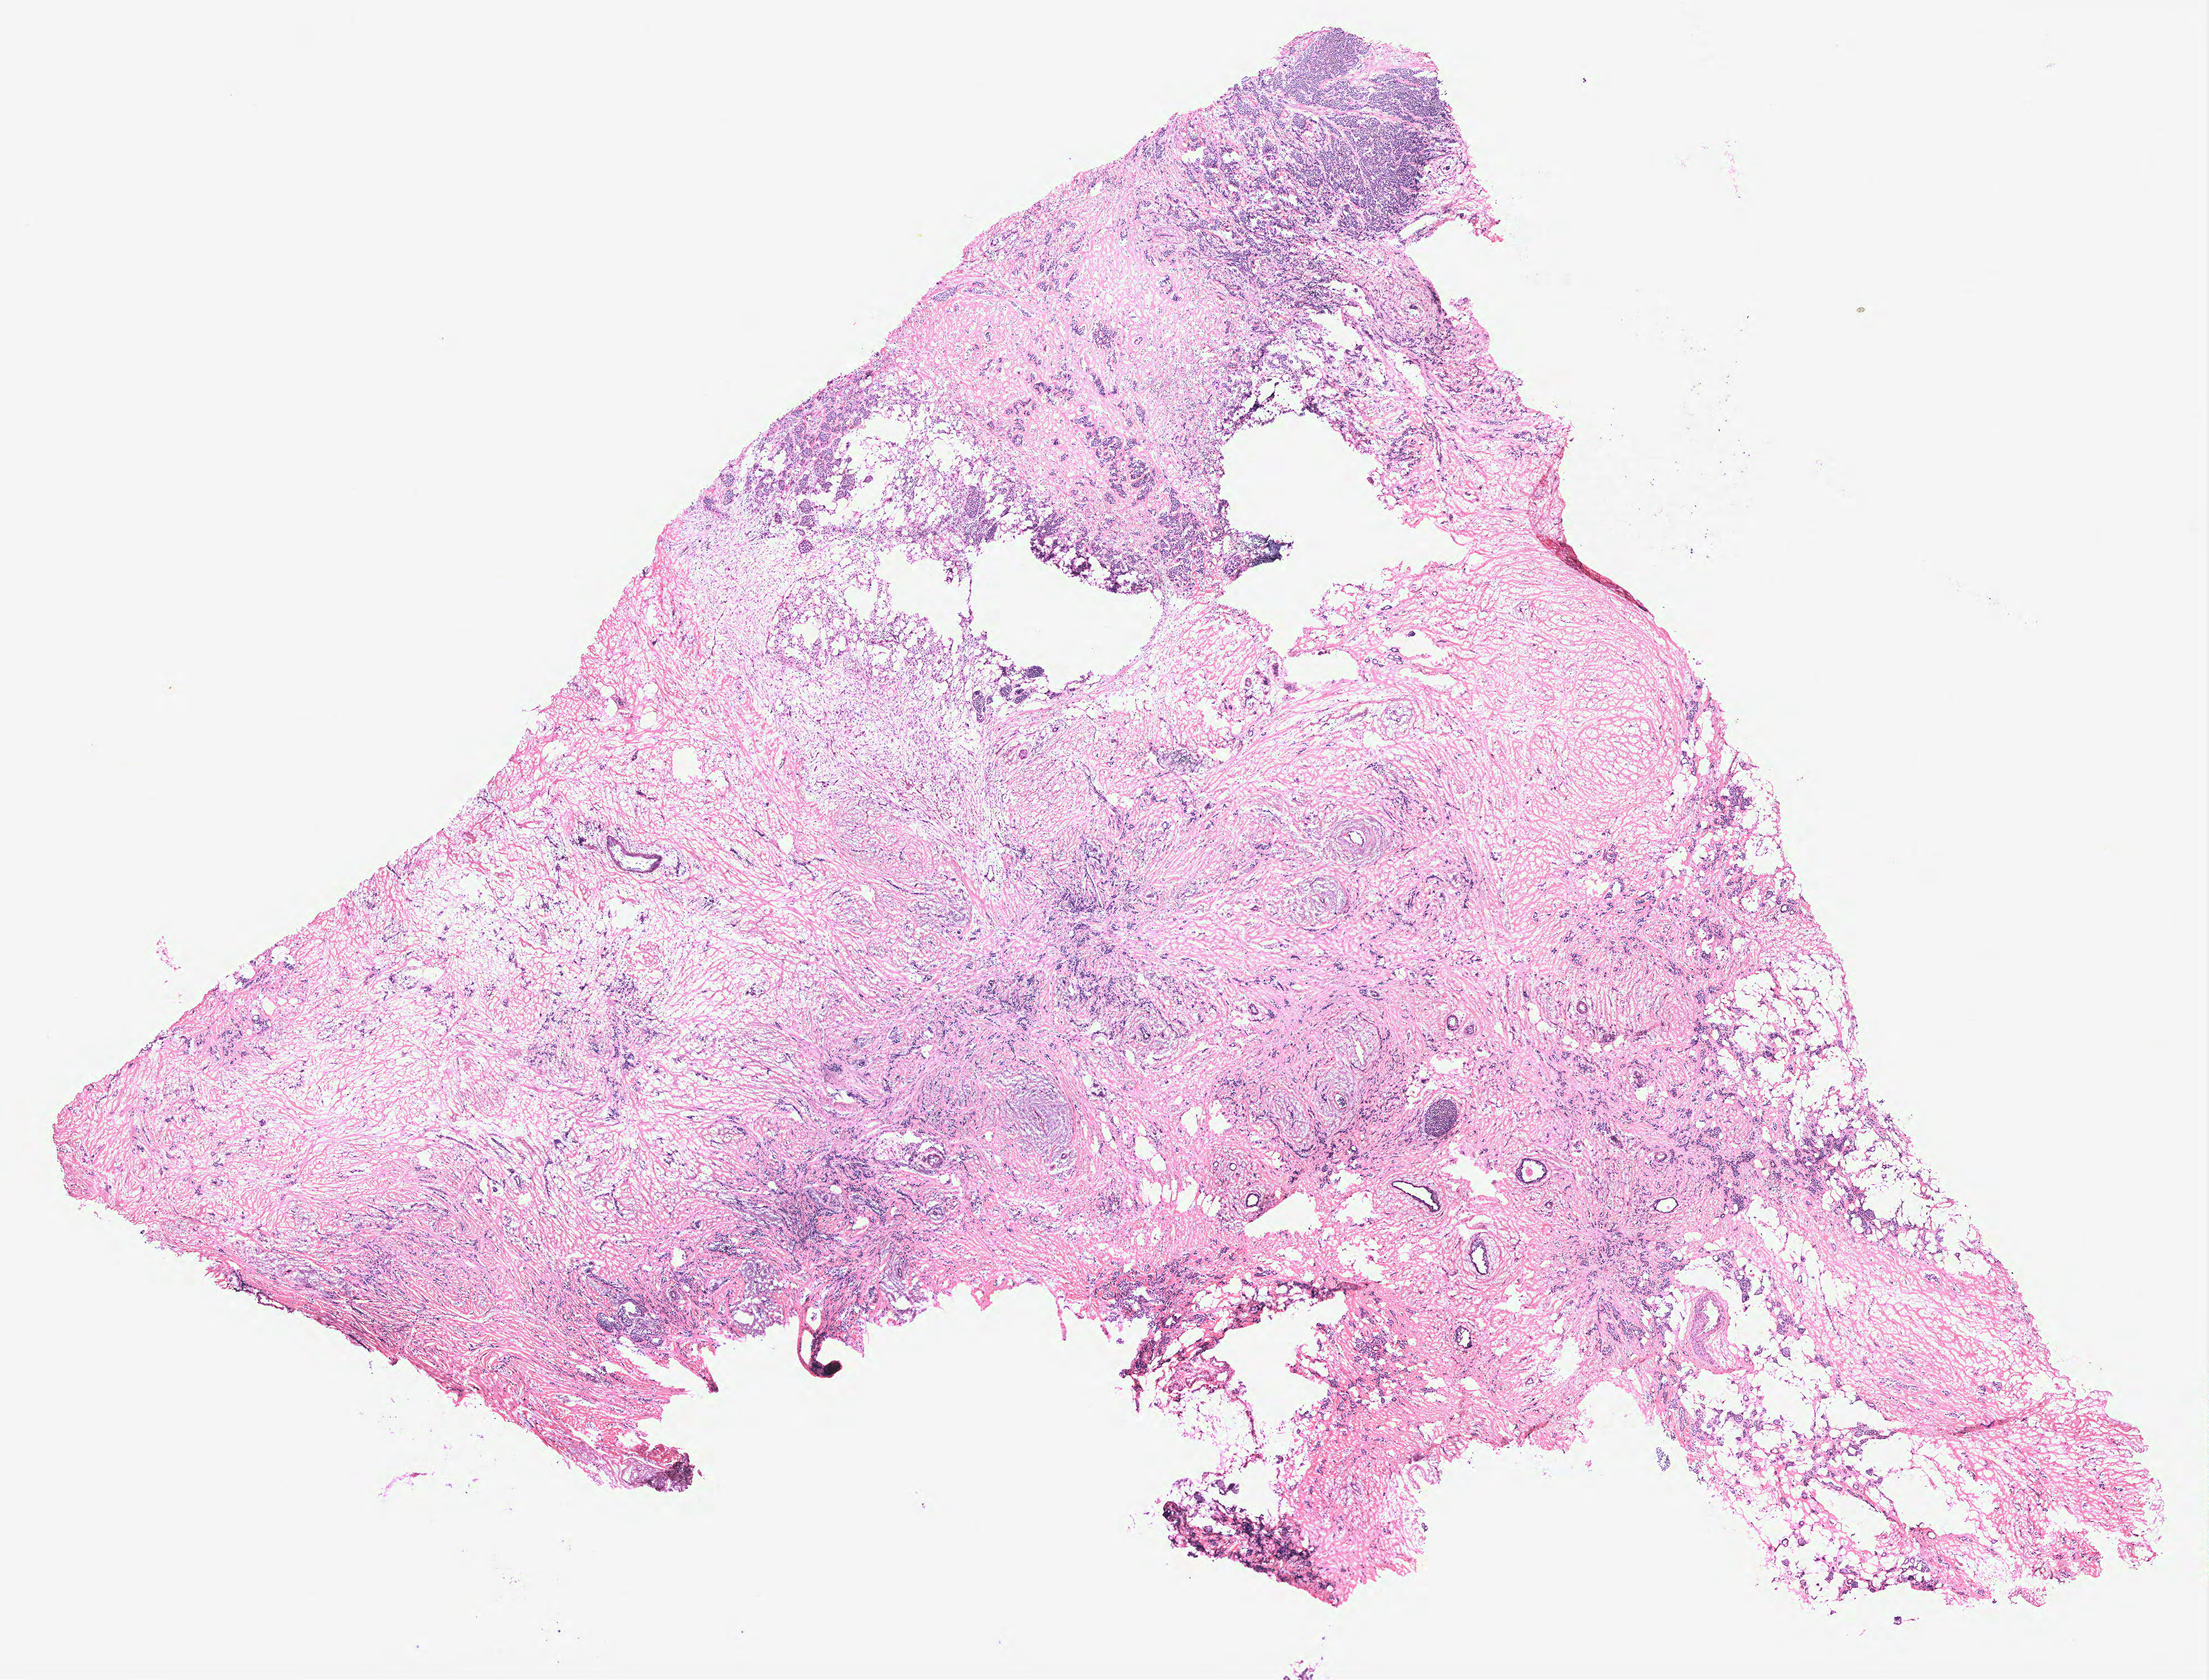
Digitized Hematoxylin and eosin (H&E) stained tissue section (whole slide) — low-resolution overview of the scanned area, about 15.8 x 12.1 mm; tumour tissue sample, breast. 70-year-old female patient.
- AJCC pathologic stage: IIIC
- histologic diagnosis: Infiltrating duct carcinoma, NOS